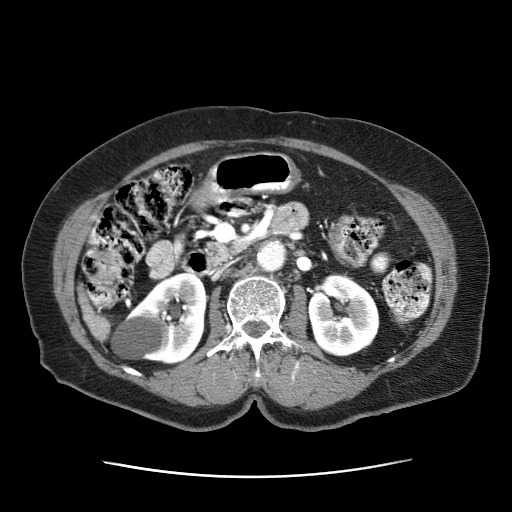
Contrast-enhanced abdominal CT (liver protocol), one axial slice; slice 8 of 63 in the series (ordered by position); reconstruction kernel STANDARD; intravenous contrast given; soft-tissue window (W 400 / L 40 HU); 512 × 512 image matrix, field of view 360 × 360 mm. Patient: female, 79 years. Case-level facts recorded for this patient, not image findings: diagnosis: hepatocellular carcinoma (patient treated with transarterial chemoembolisation; whether this scan precedes or follows treatment is not stated here); TNM stage (as recorded): Stage-II; Child-Pugh class: B; tumour differentiation: well differentiated; tumour nodularity: multinodular.
Structures marked on this image (semi-automatic segmentation, software-assisted and operator-edited):
- abdominal aorta: bounding box <257,240,287,271> (left, top, right, bottom; pixels)
- liver parenchyma outside the tumour (the mass and vessels are separate outlines, so this box may not span the whole liver): <81,299,110,341>